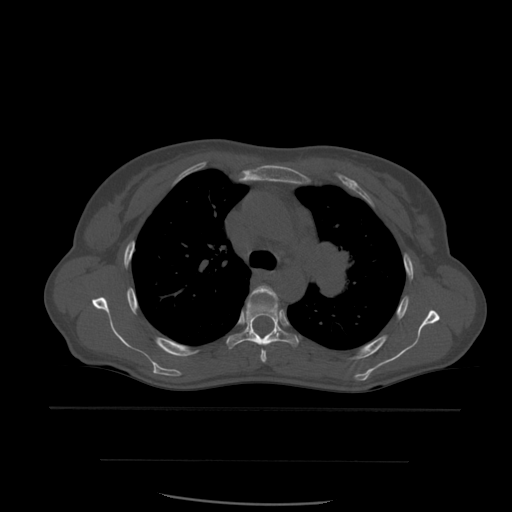
CT including the spine, one axial slice; position 414 of 574 along the scan axis; bone window (W 1800 / L 400 HU); 1.25 mm slice thickness; 512 × 512 image matrix, field of view 392 × 392 mm. Patient age 48 years. Case-level facts recorded for this patient, not image findings: primary cancer: lung.
Annotated regions visible in this slice (semi-automatic segmentation, software-assisted and operator-edited):
- T4 vertebra: box from (x=251, y=286) to (x=278, y=363) px
- T5 vertebra: (x=227, y=294)–(x=299, y=349)